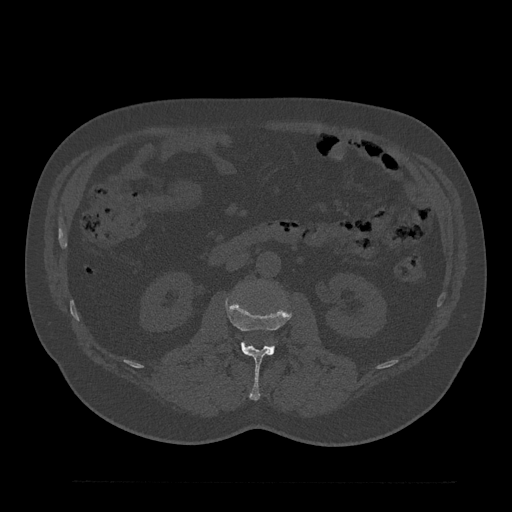
CT including the spine, one axial slice. Position 86 of 797 along the scan axis. Reconstruction kernel Br40s/3. 120 kVp. Bone window (W 1800 / L 400 HU). 0.5 mm slice thickness. 512 × 512 image matrix, field of view 430 × 430 mm. Patient: male, 61 years. Case-level facts recorded for this patient, not image findings: primary cancer: prostate.
Outlined on this slice (semi-automatic segmentation, software-assisted and operator-edited):
- L2 vertebra: bounding box (x1, y1, x2, y2) in pixels: (226, 298, 291, 400)